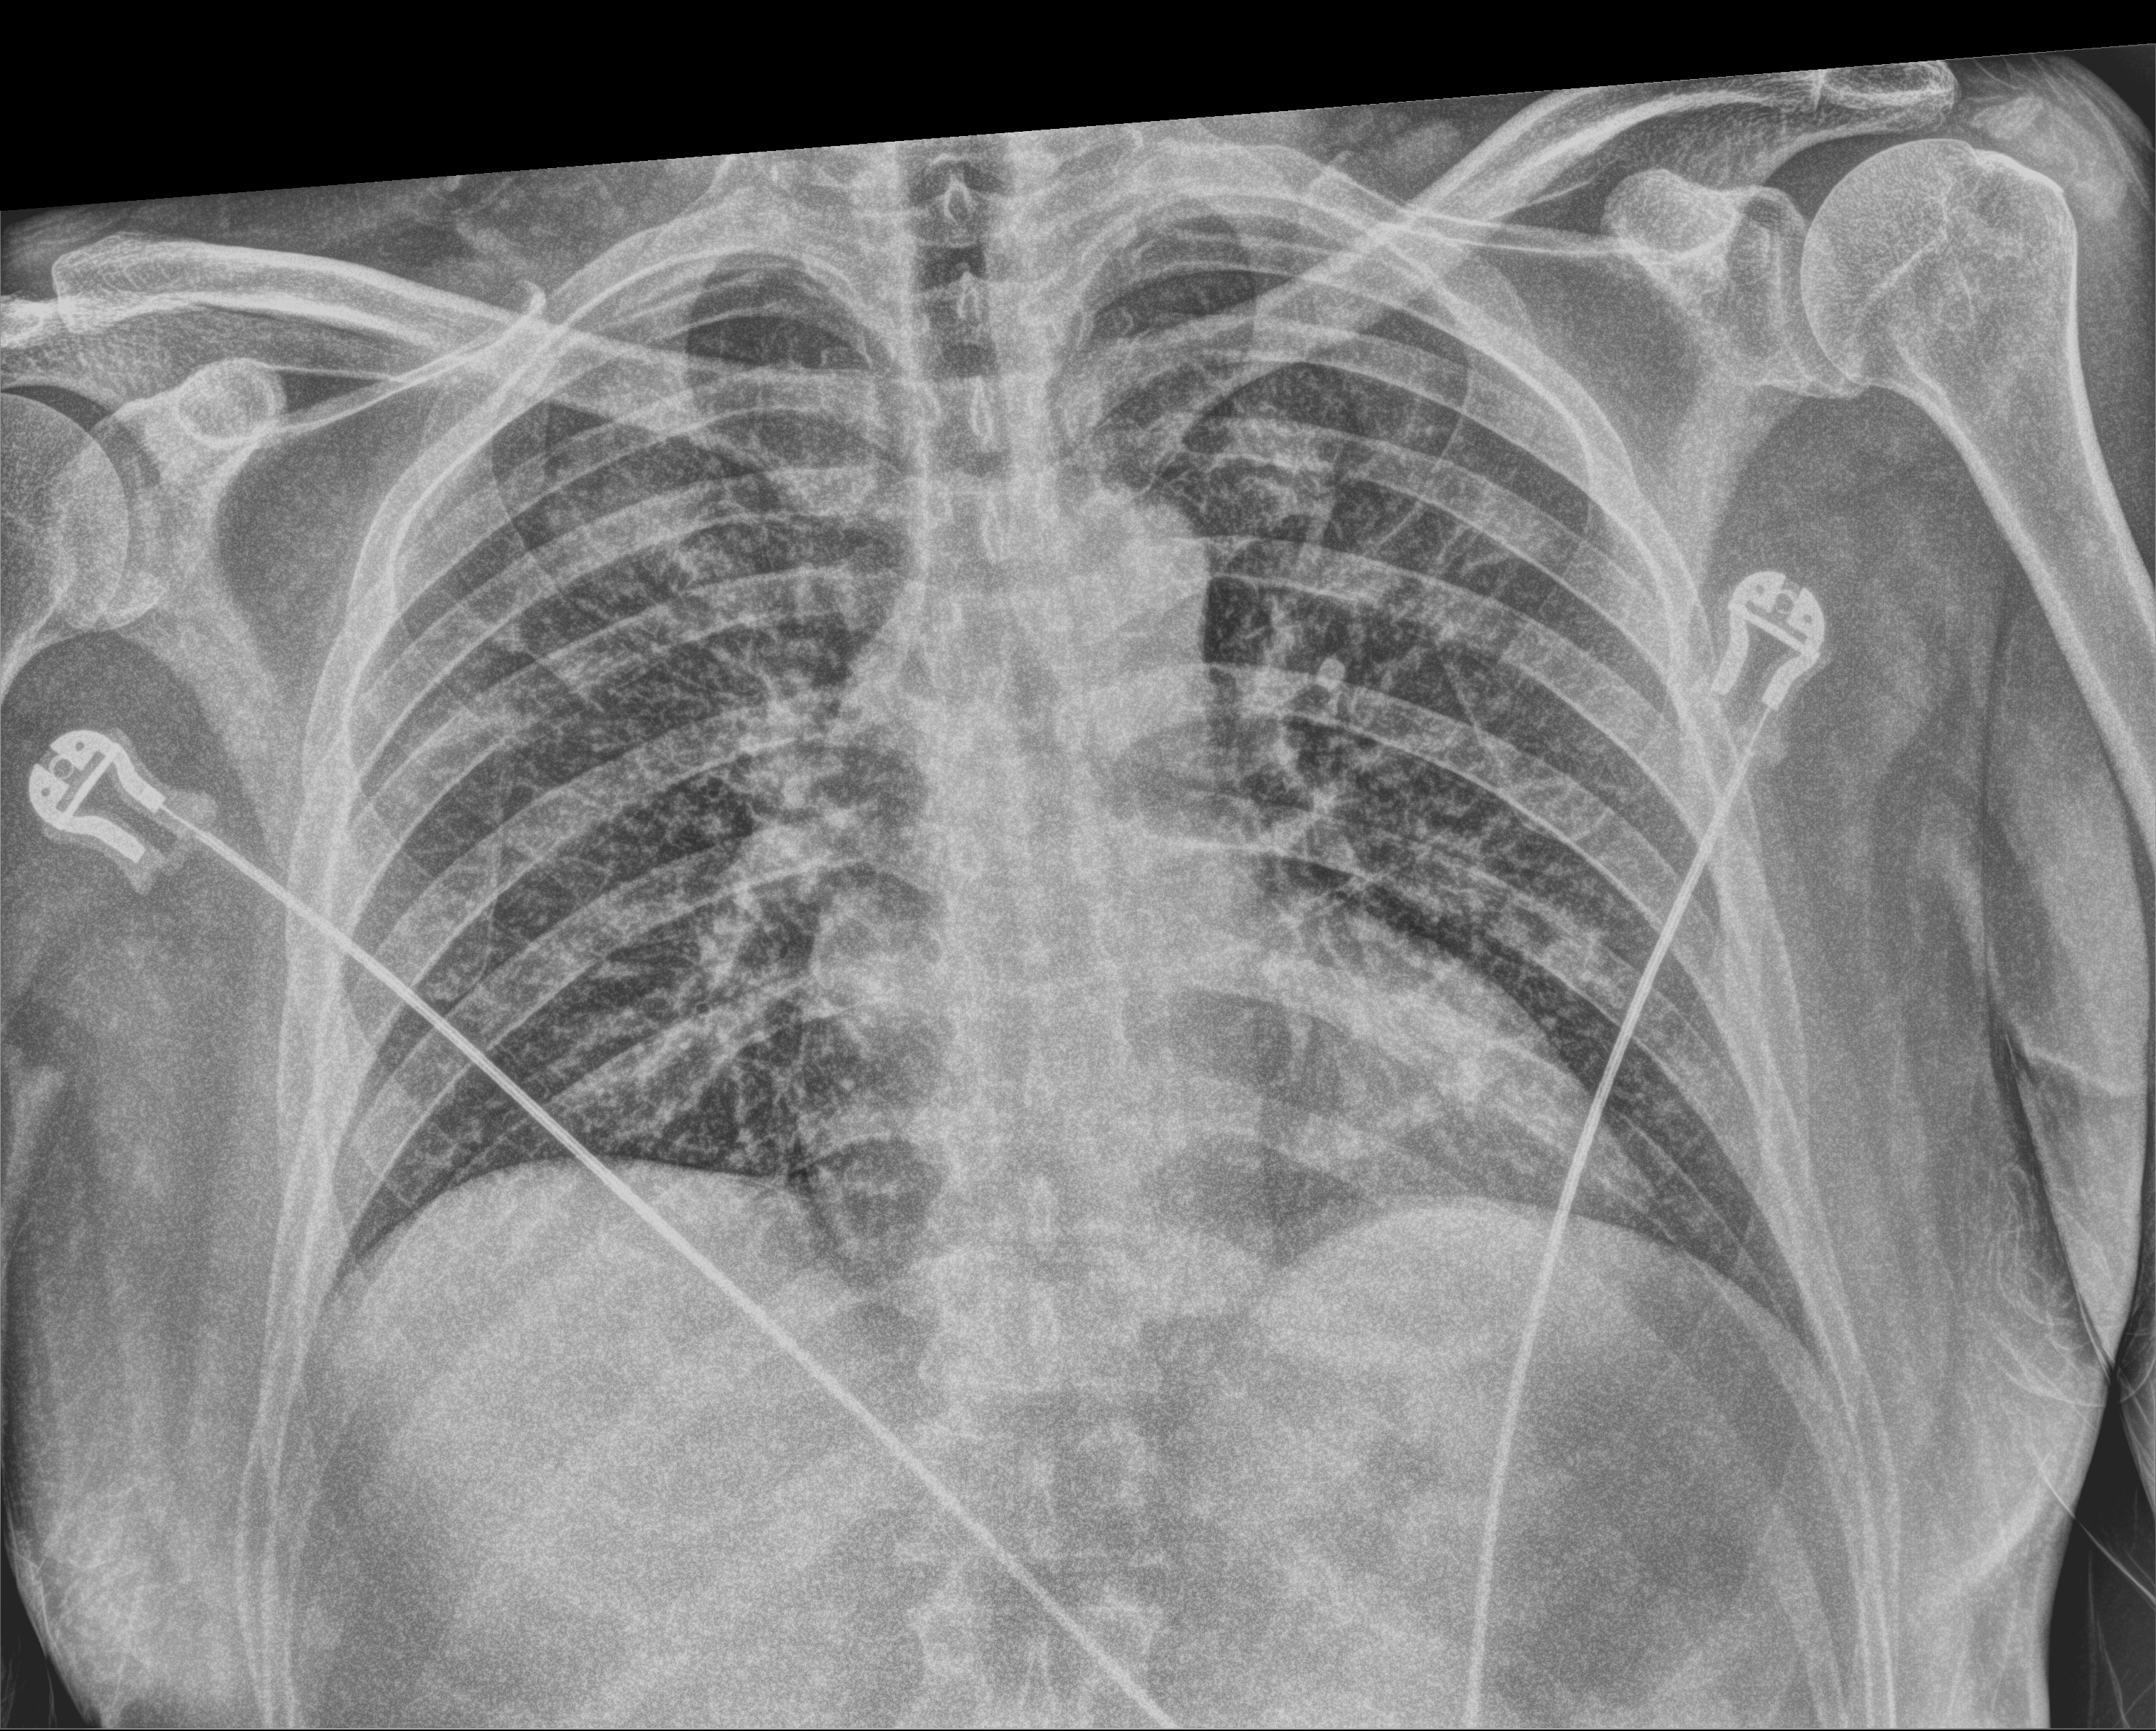
Chest X-ray (portable). Patient hospitalised with COVID-19; male, aged 18–59 years.
Hospital-stay facts (about this admission, not read from this image; timing relative to this image not recorded): mechanically ventilated during this hospital stay: no; smoking status (admission record): never; admitted to intensive care during this hospital stay: no.